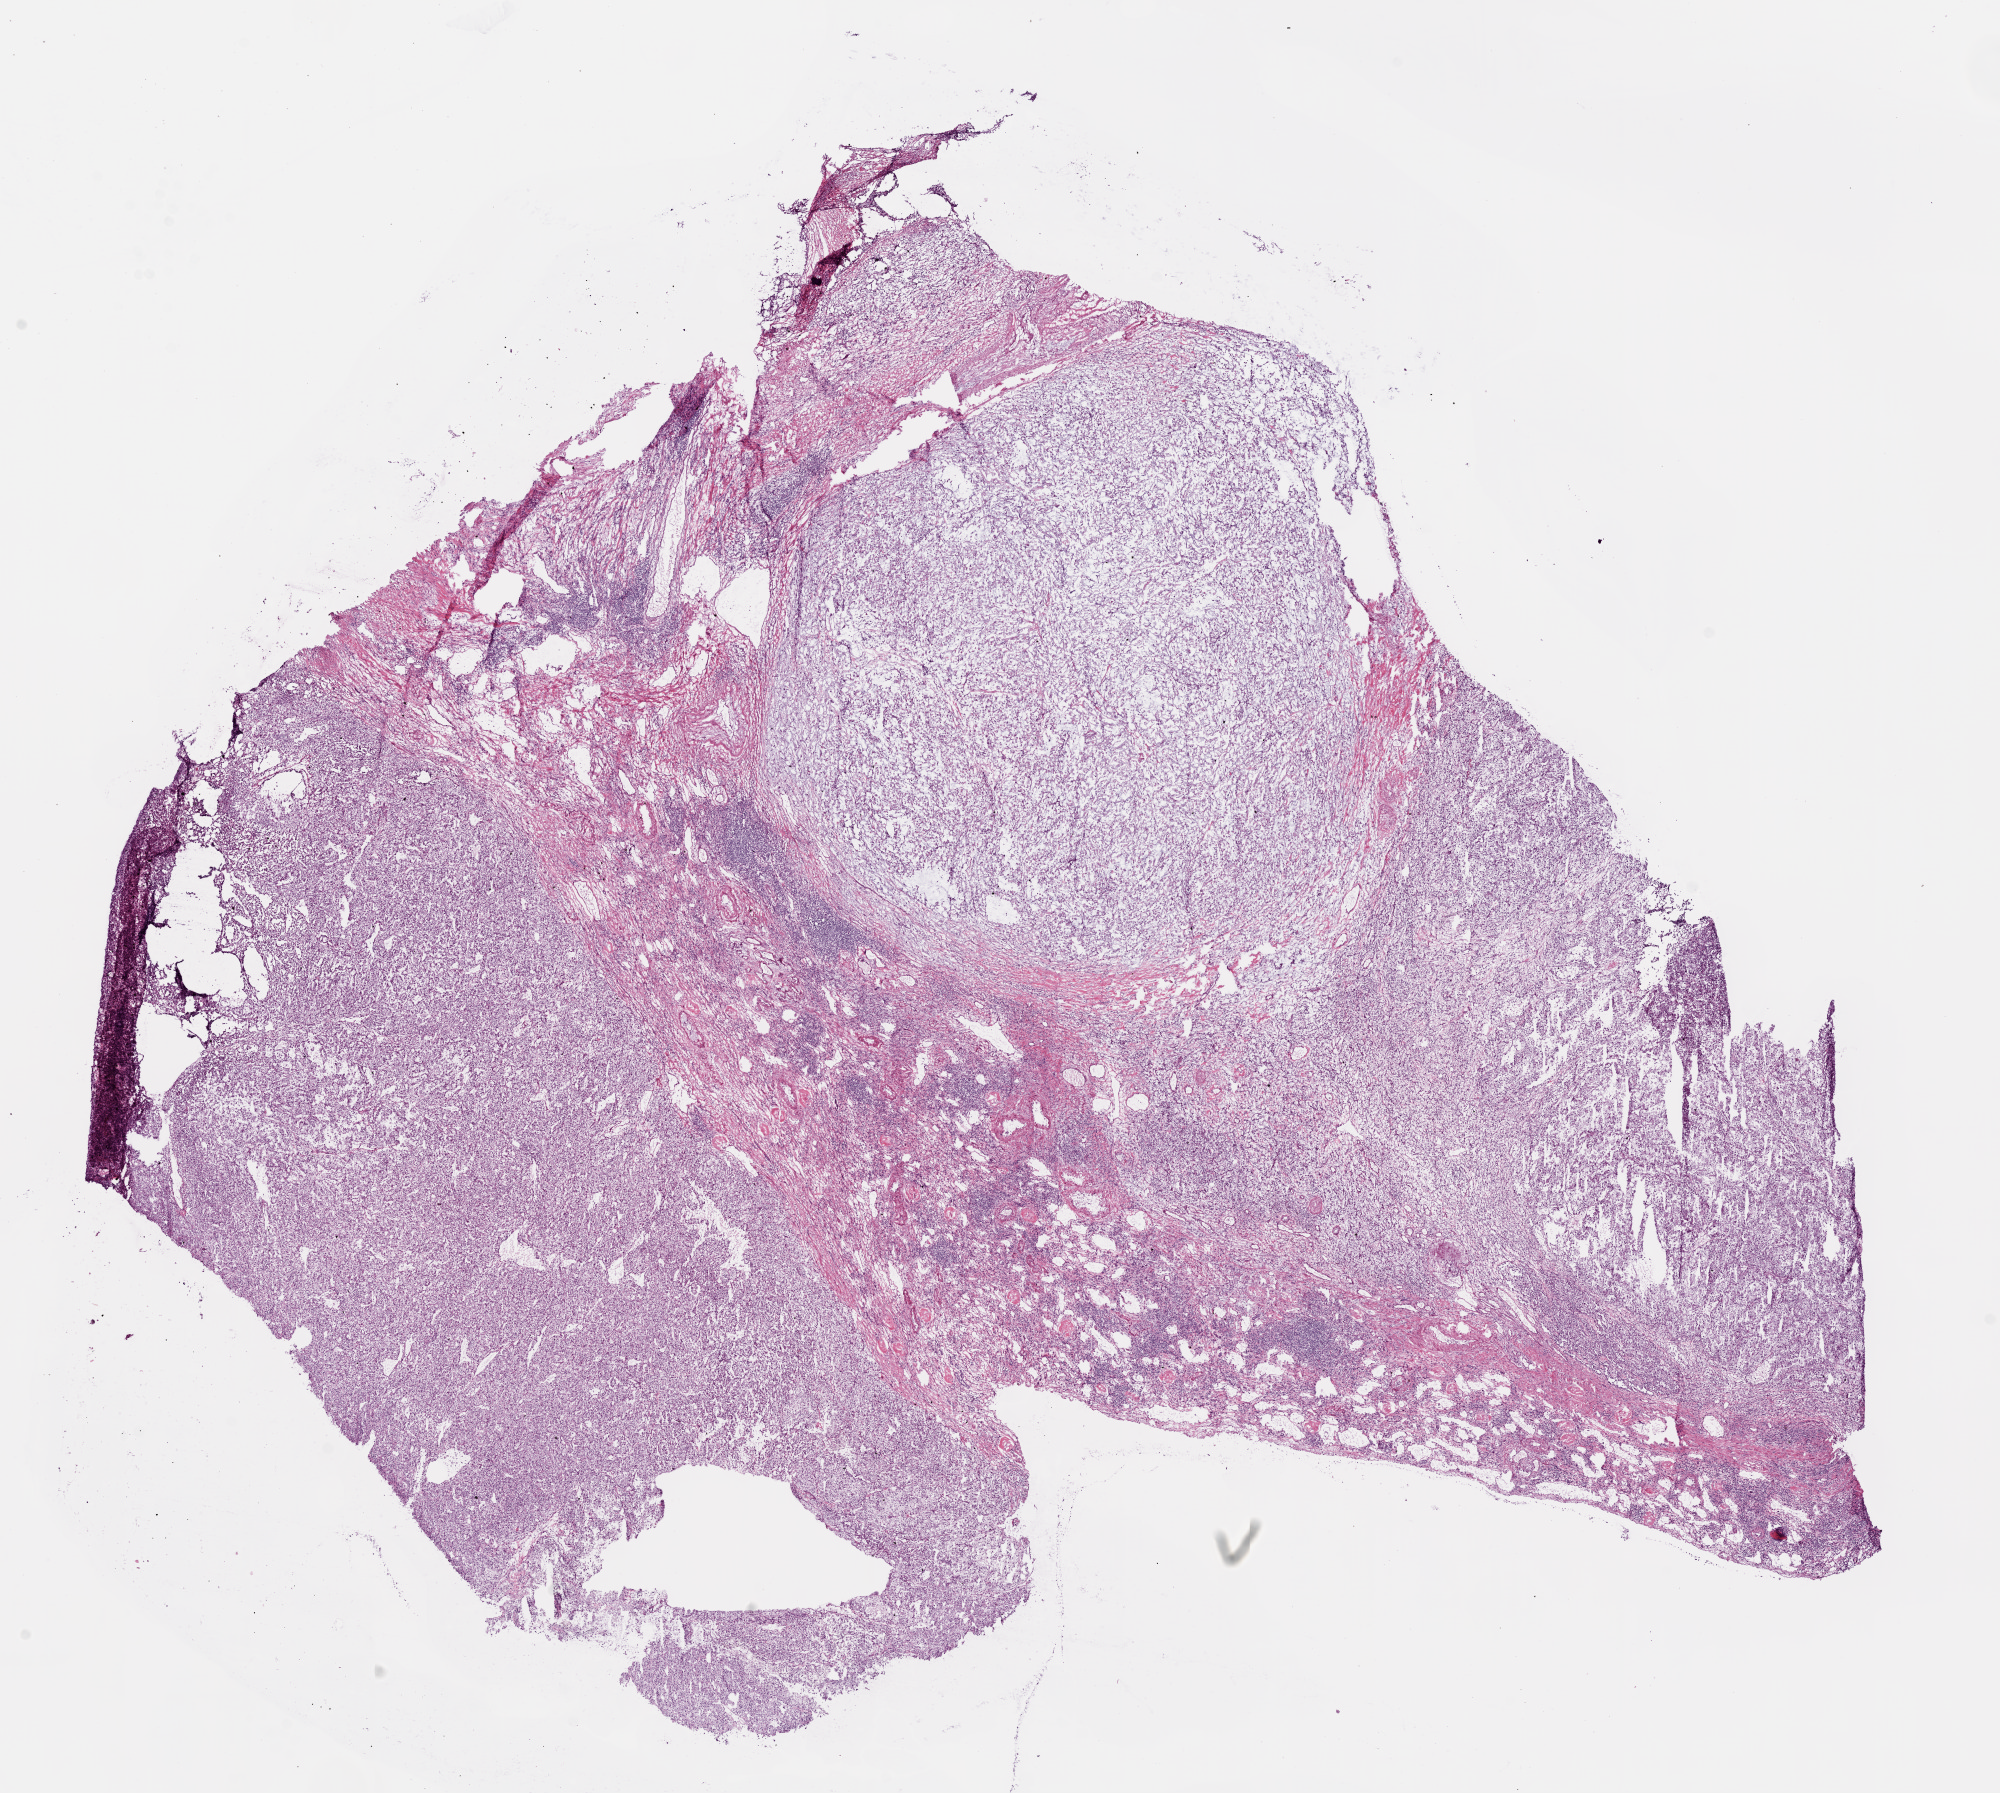
Hematoxylin and eosin (H&E) stained whole-slide image, shown as a low-resolution overview of the whole scanned area (about 16.0 x 14.4 mm, acquisition: 20x scan), frozen section from the bottom of the tissue portion, kidney, primary tumour sample. Female, age 62 years at initial diagnosis. Histologic grade: G3 (poorly differentiated). Slide review estimates, as recorded: tumour cells 75%, tumour nuclei 80%, normal cells 0%, stromal cells 25%, necrosis 0%.
Histologic diagnosis: Clear cell adenocarcinoma, NOS. AJCC pathologic stage: III (6th edition).